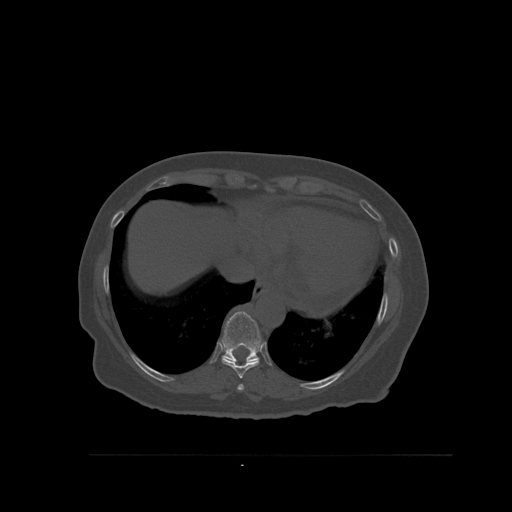
CT including the spine, one axial slice; position 329 of 527 along the scan axis; bone window (W 1800 / L 400 HU); 1.5 mm slice thickness; 512 × 512 image matrix, field of view 470 × 470 mm. Female patient, age 73 years. Case-level facts recorded for this patient, not image findings: primary cancer: breast; vertebrae with lytic lesions (as recorded): L2.
Outlined on this slice (semi-automatically segmented with operator editing):
- T10 vertebra: bounding box [x1, y1, x2, y2] px = [222, 311, 262, 362]
- T8 vertebra: [237, 384, 244, 391]
- T9 vertebra: [222, 342, 262, 379]